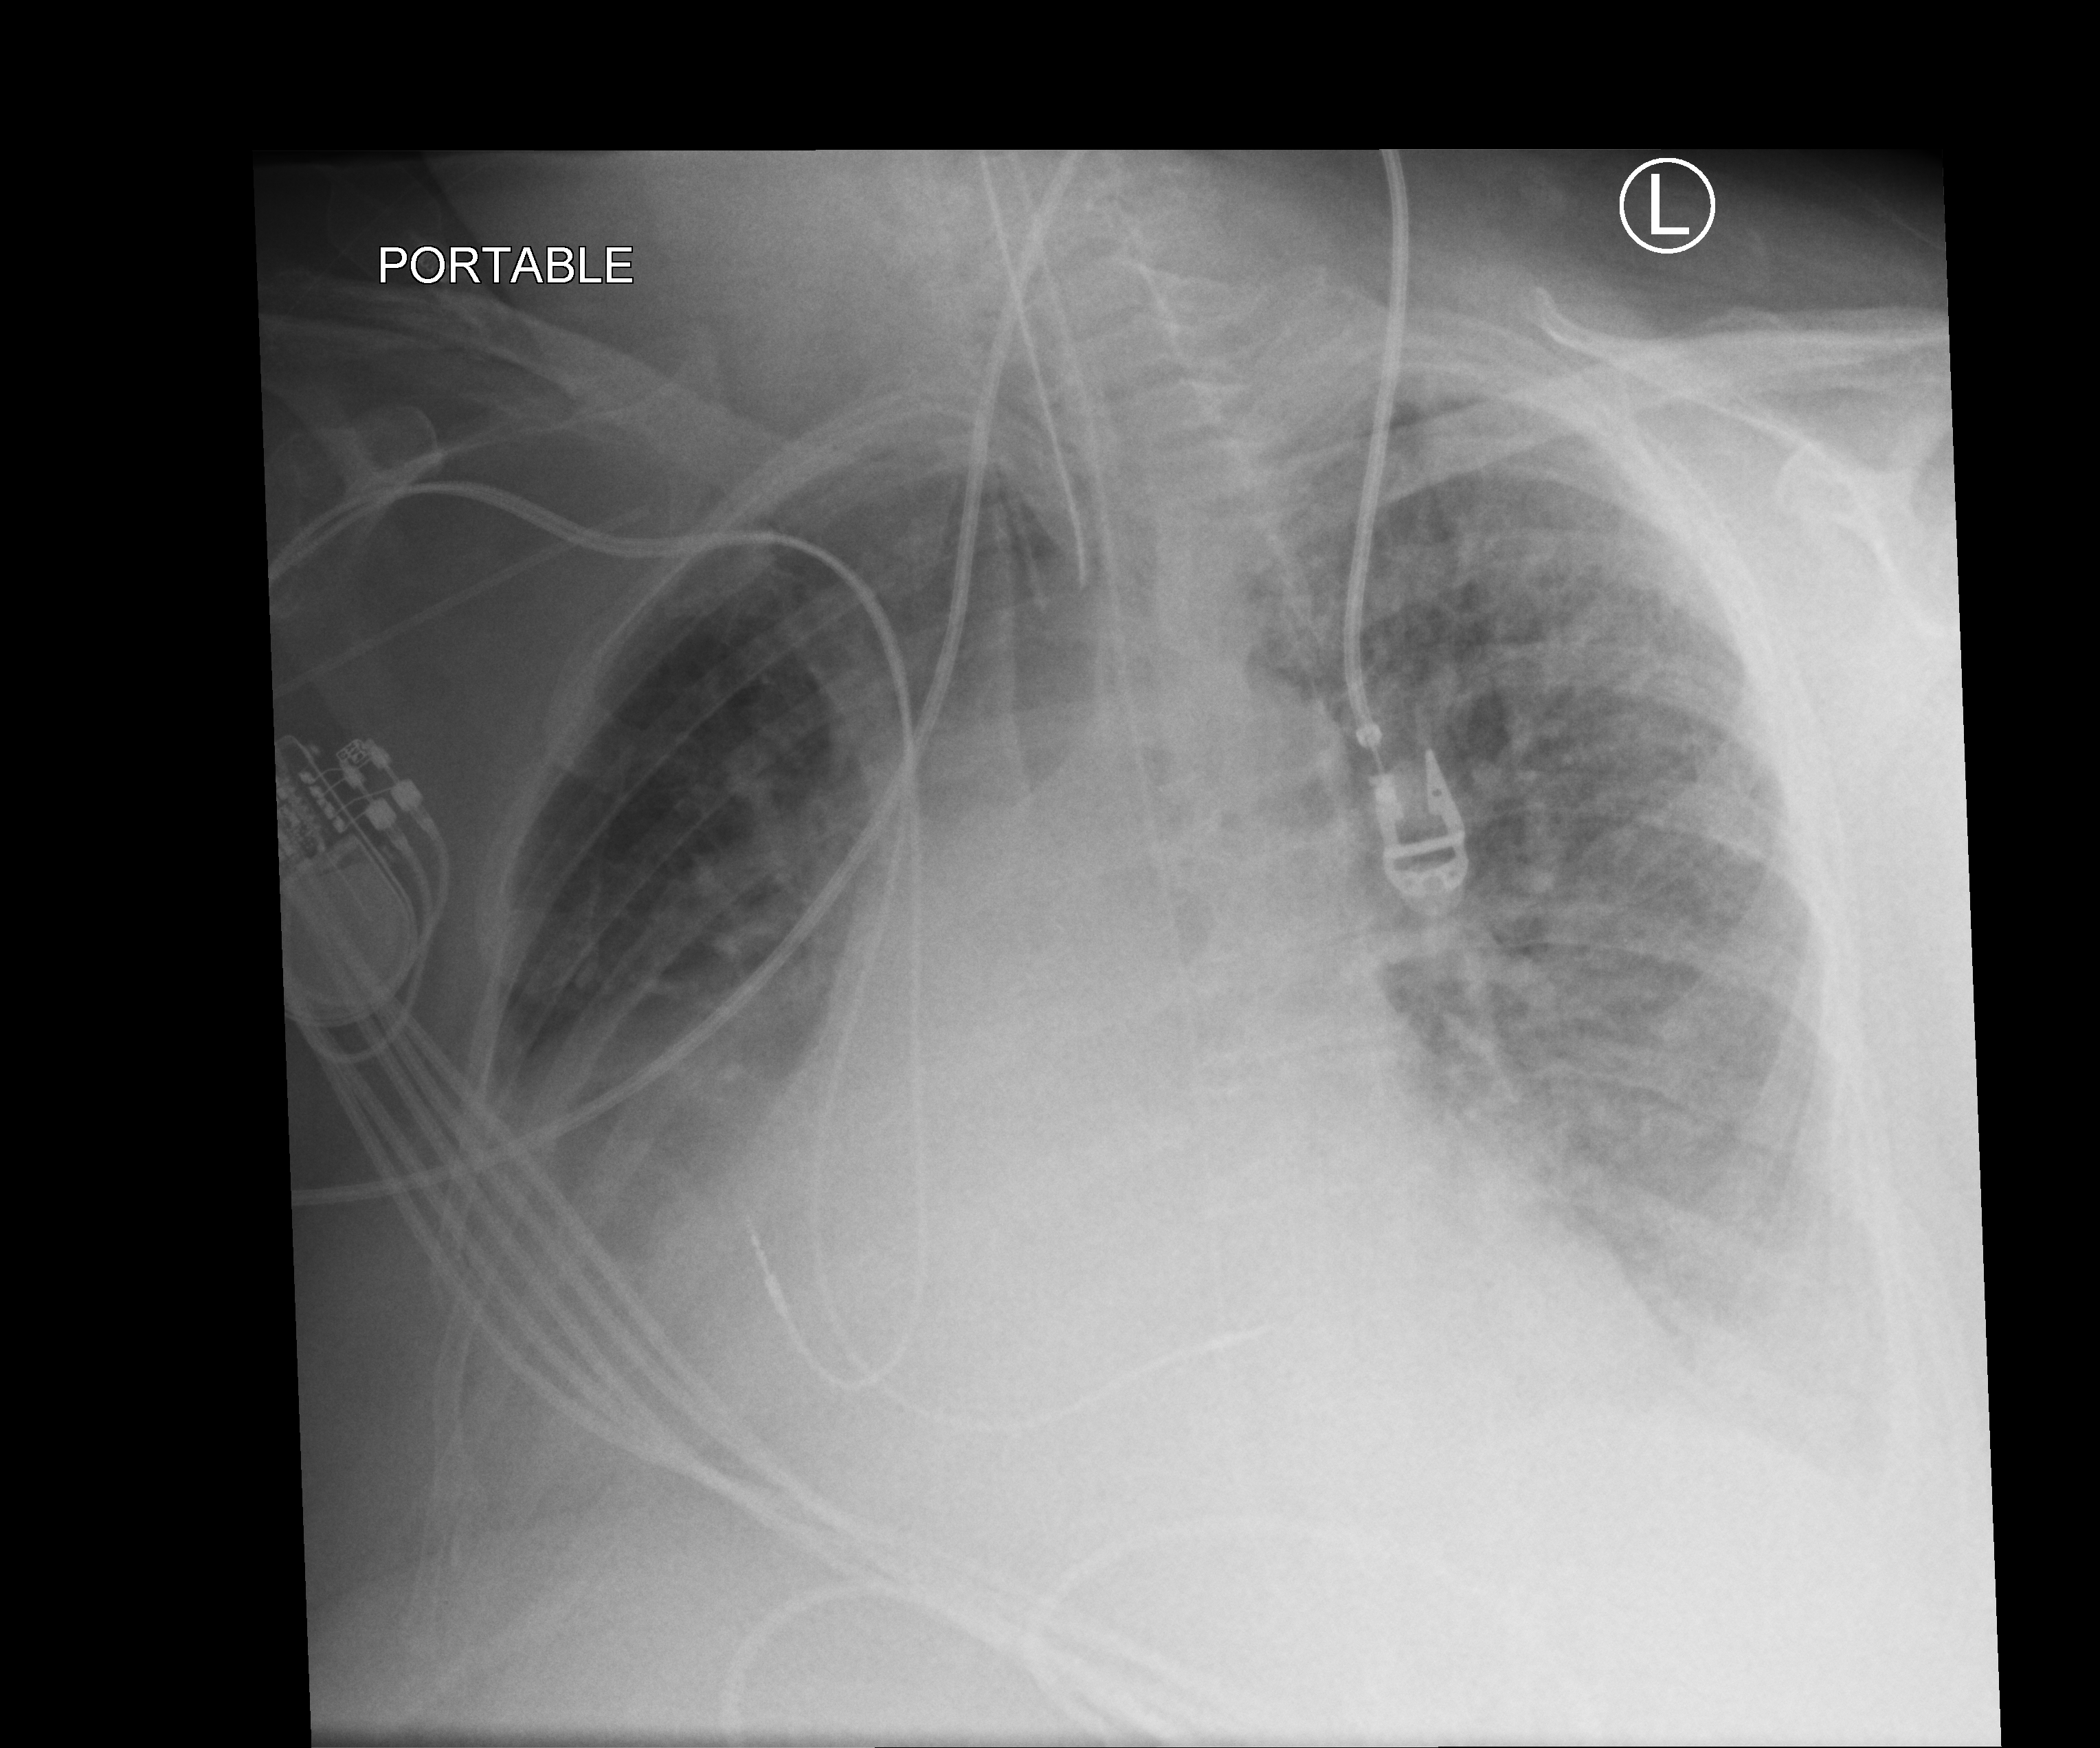
Bedside chest radiograph (computed radiography); anteroposterior (AP) projection. Female patient hospitalised with COVID-19, age 75–90 years.
Admission-level facts for this patient (not findings on this image; timing relative to this image not recorded):
- length of hospital stay: 21 days
- mechanically ventilated during this hospital stay: yes
- chronic kidney disease (admission record): yes